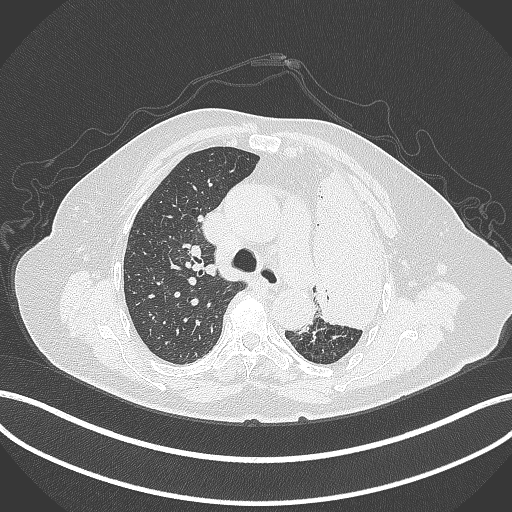
Chest CT, one axial slice; slice 268 of 399 in the series (ordered by position); reconstruction kernel B70f; lung window (W 1500 / L -600 HU); 1 mm slice thickness; 512 × 512 image matrix, field of view 400 × 400 mm. Patient: female, 75 years. Case-level facts recorded for this patient, not image findings: clinical TNM (as recorded): T3 N3 M1.
Annotated regions visible in this slice (bounding box drawn by a radiologist):
- lung tumour (recorded histology: adenocarcinoma): bounding box <307,159,387,335> (left, top, right, bottom; pixels)